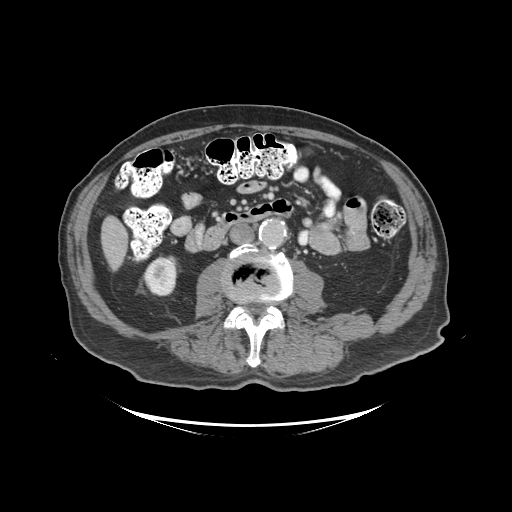
Contrast-enhanced abdominal CT (liver protocol), one axial slice. Position 25 of 99 along the scan axis. 140 kVp. Soft-tissue window (W 400 / L 40 HU). 2.5 mm slice thickness. 512 × 512 image matrix, field of view 460 × 460 mm. Case-level facts recorded for this patient, not image findings: diagnosis: hepatocellular carcinoma (patient treated with transarterial chemoembolisation; whether this scan precedes or follows treatment is not stated here); TNM stage (as recorded): Stage-I; Child-Pugh class: A; tumour differentiation: moderately differentiated; tumour nodularity: uninodular.
Annotated regions visible in this slice (semi-automatically segmented with operator editing):
- liver parenchyma outside the tumour (the mass and vessels are separate outlines, so this box may not span the whole liver): bounding box [x1, y1, x2, y2] px = [100, 216, 128, 270]